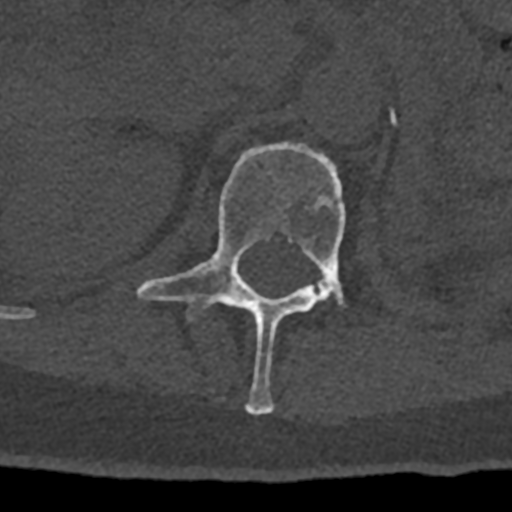
CT including the spine, one axial slice. Position 434 of 797 along the scan axis. Reconstruction kernel Br40s/3. Bone window (W 1800 / L 400 HU). 0.5 mm slice thickness. 512 × 512 image matrix. Male patient, age 74 years. Case-level facts recorded for this patient, not image findings: primary cancer: renal; vertebrae with lytic lesions (as recorded): T10, L1, L2, L3, L4, L5.
Structures marked on this image (semi-automatically segmented with operator editing):
- L1 vertebra: bounding box <137,142,346,415> (left, top, right, bottom; pixels)